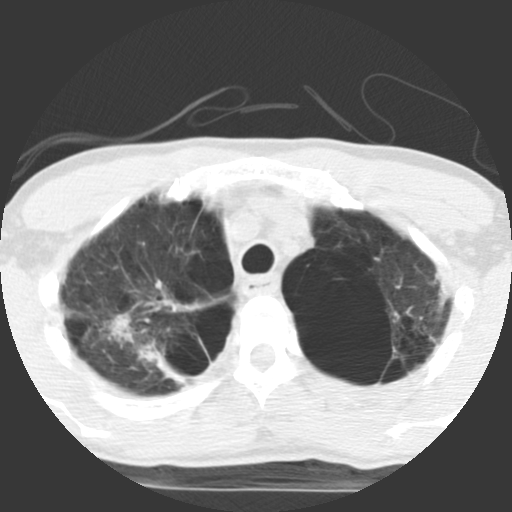
Low-dose screening chest CT, axial slice; baseline screening round; lung window (W 1500 / L -600 HU); standard (soft-tissue) reconstruction kernel (STANDARD); 512 × 512 image matrix, field of view 270 × 270 mm. Male, age 62 years at enrolment. Current smoker at enrolment.
Expert reader's lesion annotation, box from (x=116, y=316) to (x=213, y=390) px. Screening reader's record for this exam: no non-calcified nodule ≥4 mm recorded. Participant outcome: lung cancer diagnosed 357 days after this screen — non-small cell carcinoma, right upper lobe, poorly differentiated (G3), stage IA (AJCC 6th edition), 70 mm at pathology.